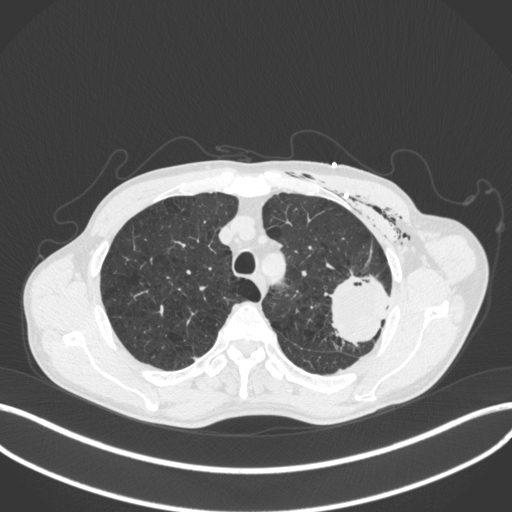
Chest CT, one axial slice; position 316 of 416 along the scan axis; reconstruction kernel B31f; lung window (W 1500 / L -600 HU); 1 mm slice thickness; 512 × 512 image matrix, field of view 400 × 400 mm. Male patient, age 58 years. From the clinical record (not read from this slice): clinical TNM (as recorded): T3 N0 M0.
Outlined on this slice (bounding box drawn by a radiologist):
- lung tumour (recorded histology: adenocarcinoma): bounding box <328,272,396,347> (left, top, right, bottom; pixels)